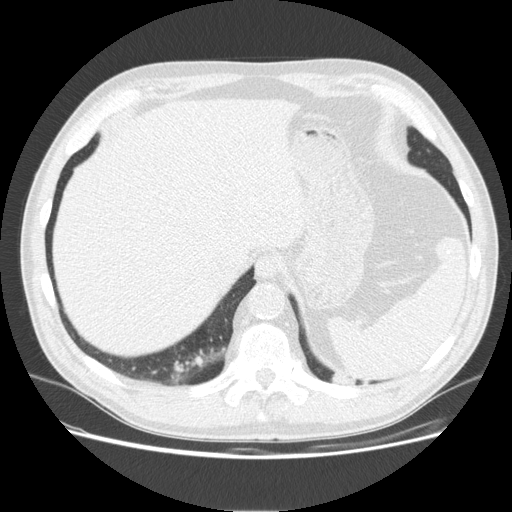
Low-dose screening chest CT, one axial slice. Slice 37 of 165 in the series (ordered by position). Lung window (W 1500 / L -600 HU). 2.5 mm slice thickness. 512 × 512 image matrix, field of view 375 × 375 mm.
Annotated regions visible in this slice (expert manual segmentation):
- lesion 1 (tumor, upper lobe of left lung): bounding box <330,373,360,385> (left, top, right, bottom; pixels)